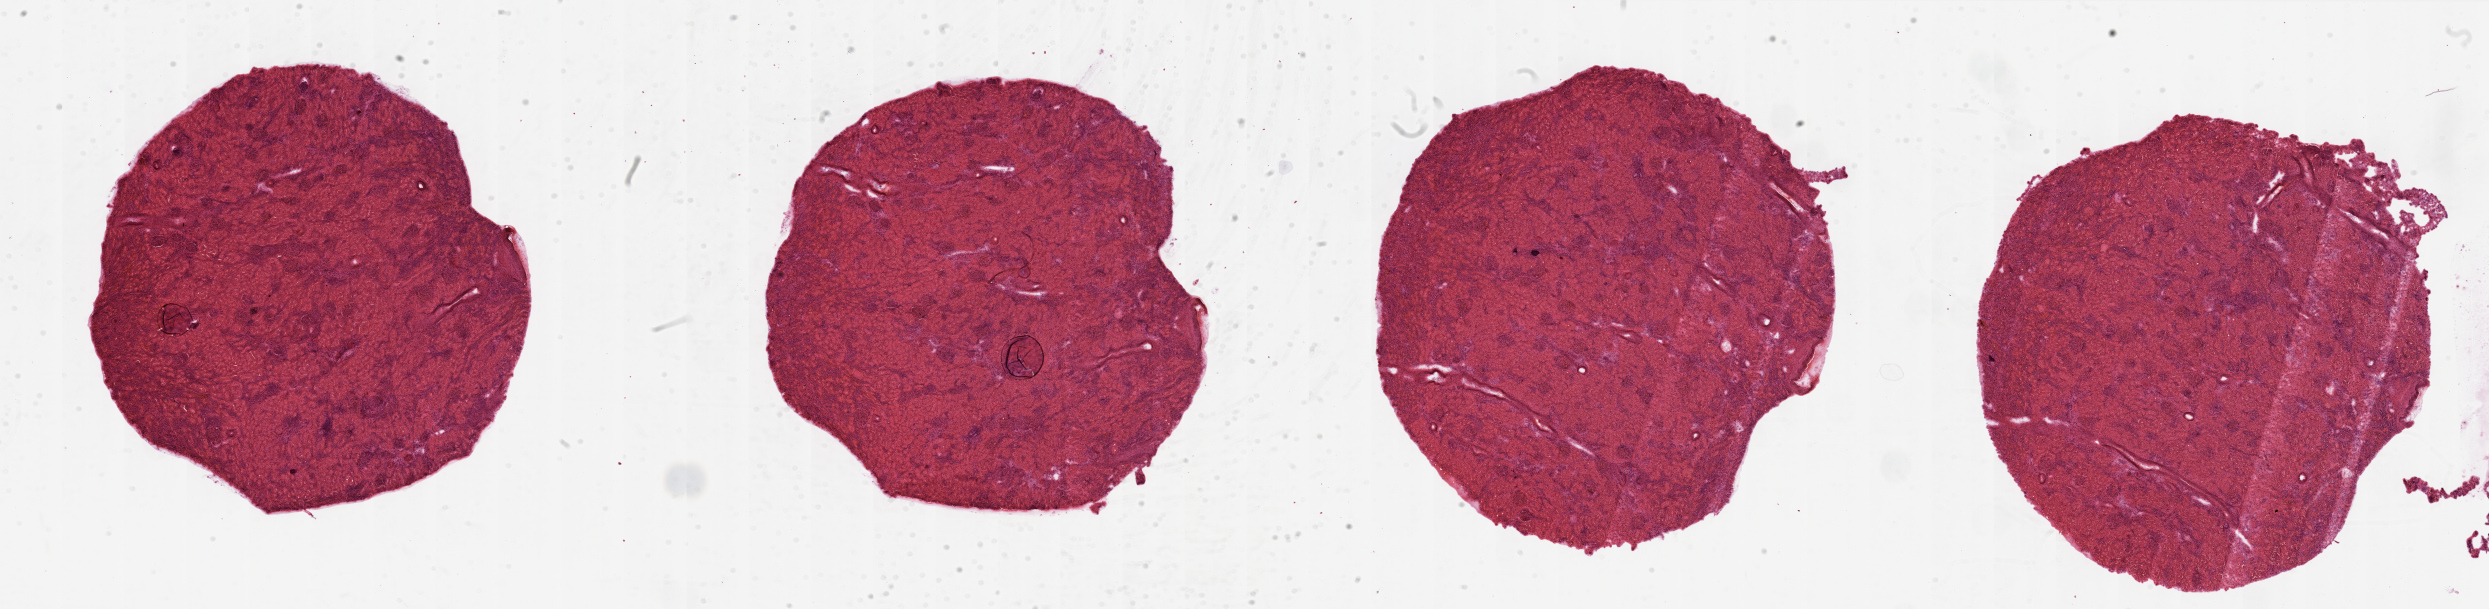
H&E whole-slide image — shown as a low-resolution overview of the whole scanned area (about 39.4 x 9.6 mm). Normal (non-tumour) tissue sample, sampled site: kidney. Patient: male, age 78 years.
• this section: normal (non-tumour) tissue from the same patient
• patient diagnosis: Renal cell carcinoma, NOS